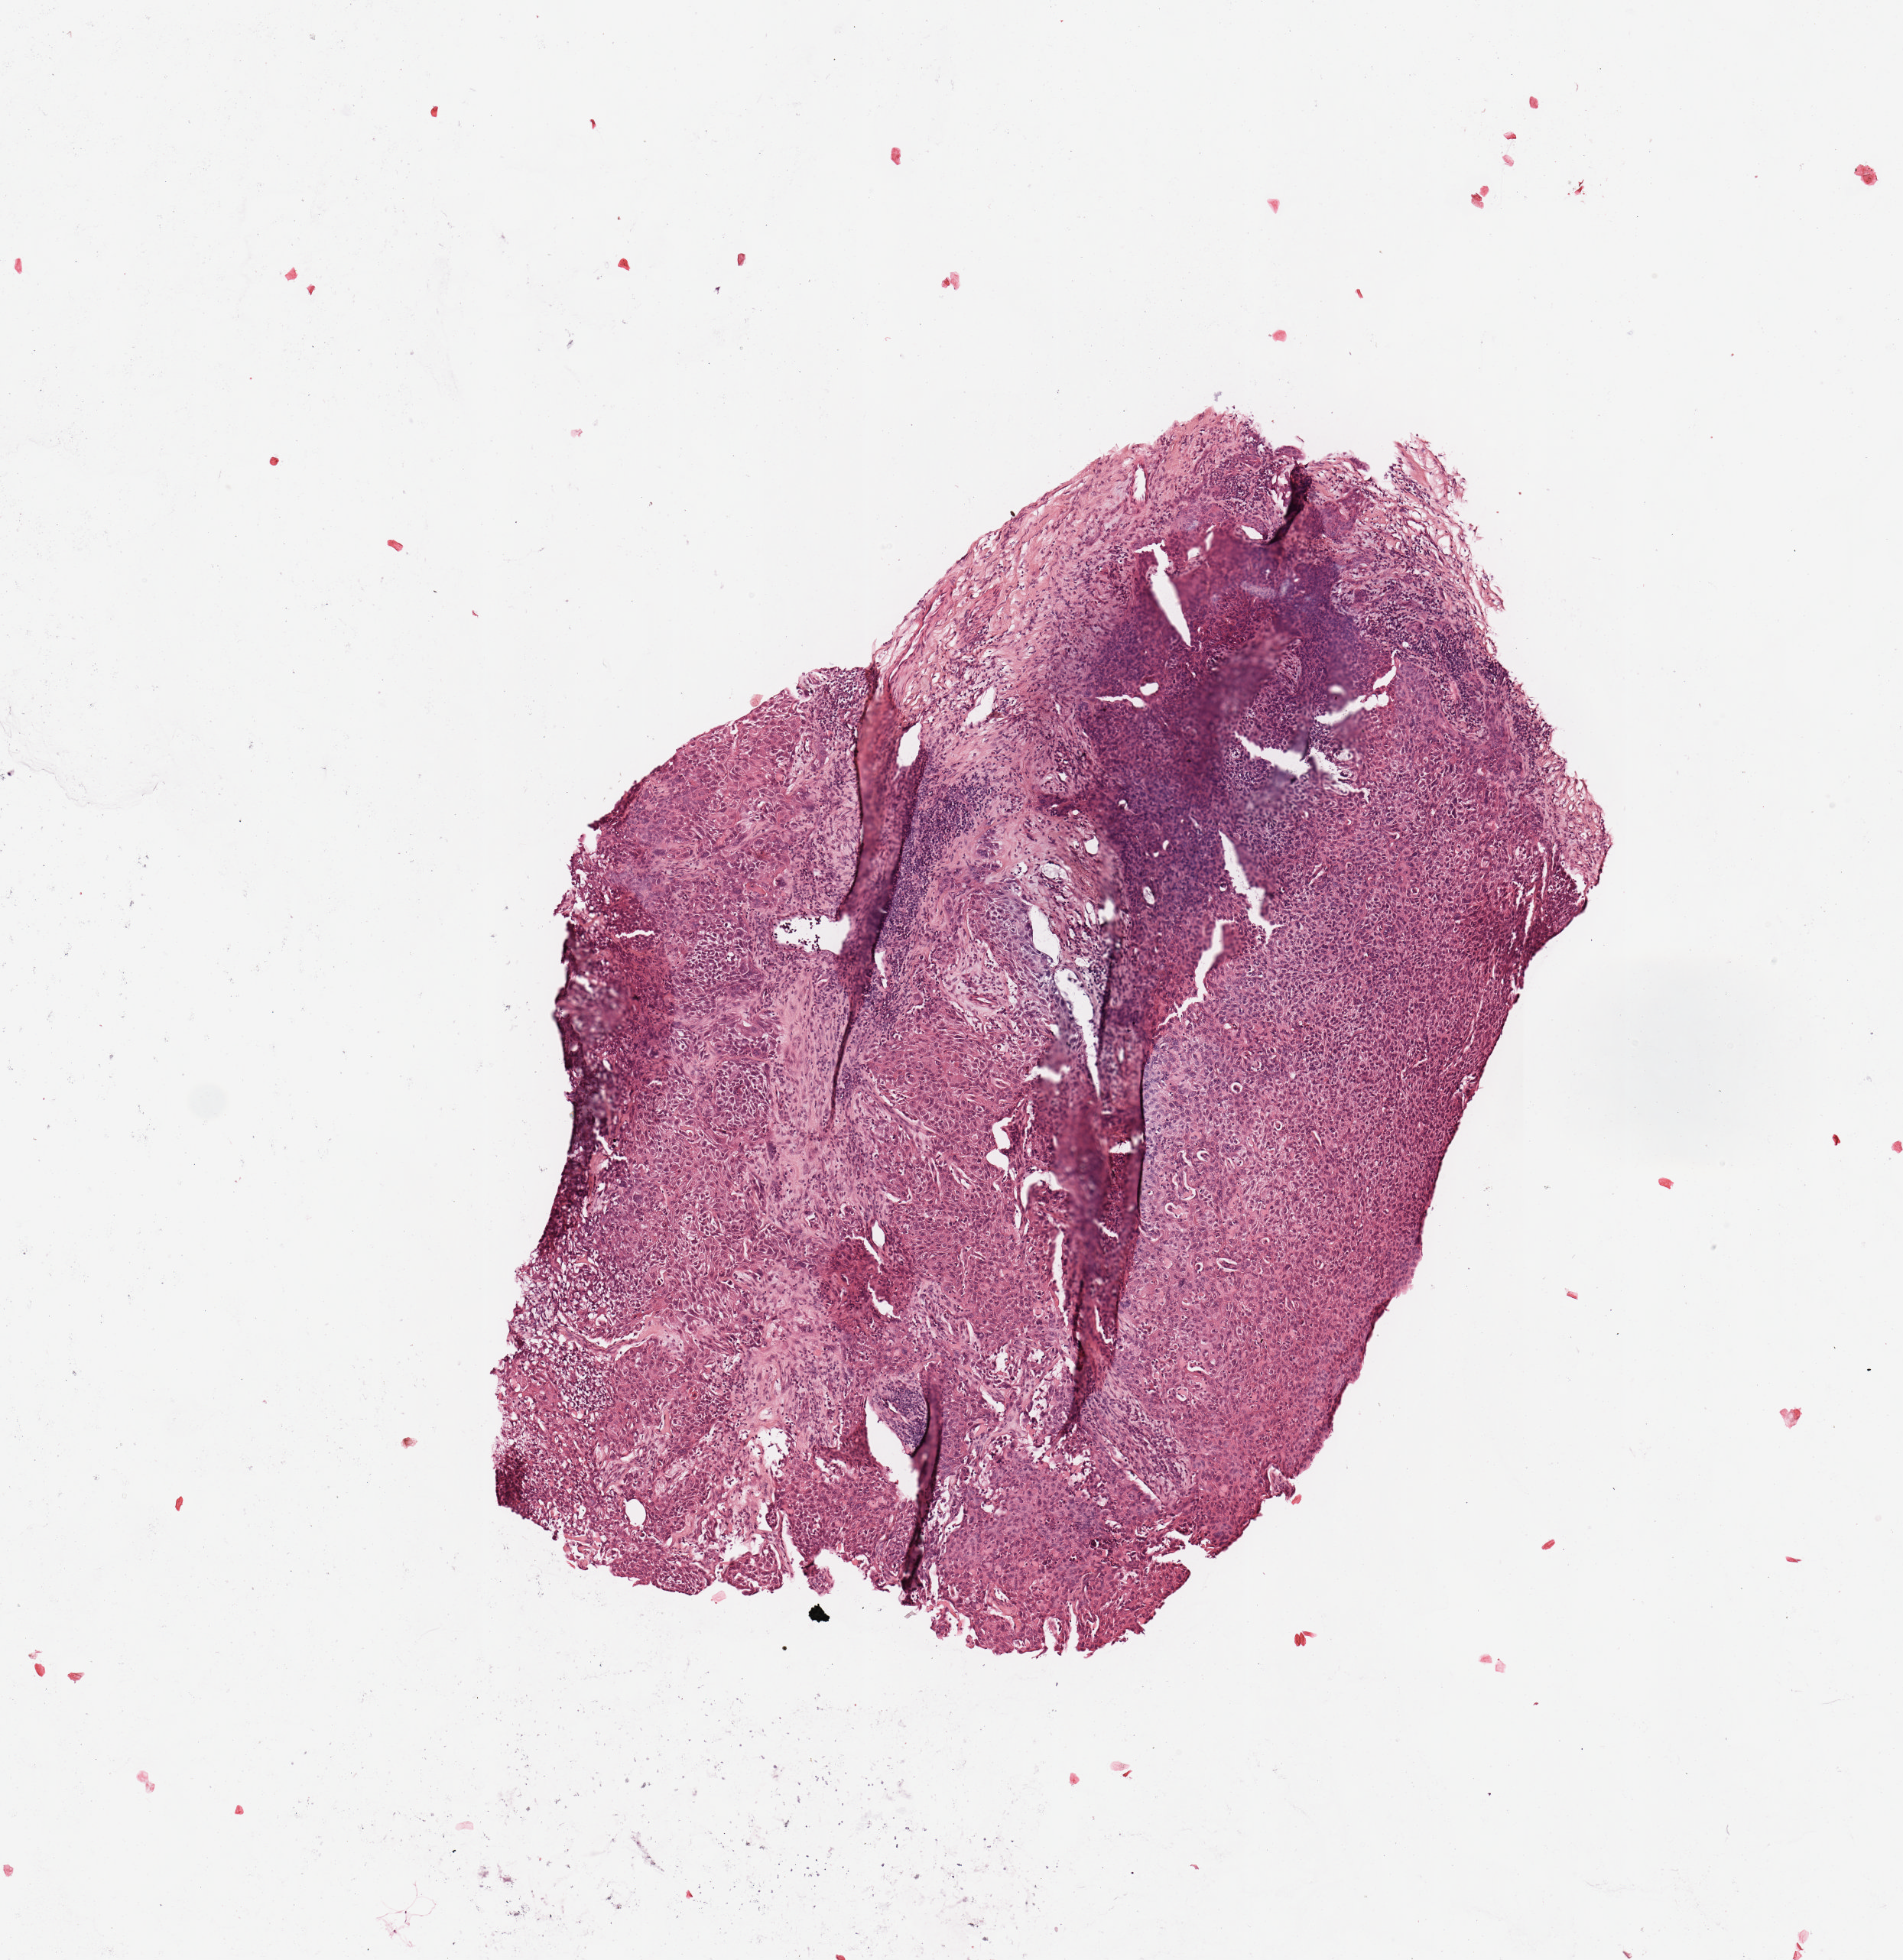
Digitized H&E tissue section (whole slide) — shown as a low-resolution overview of the whole scanned area (about 4.9 x 5.1 mm, slide scanned at 20x). Head and neck, tissue type not recorded. 53-year-old female patient.
Patient diagnosis: Squamous cell carcinoma, NOS (larynx, NOS).